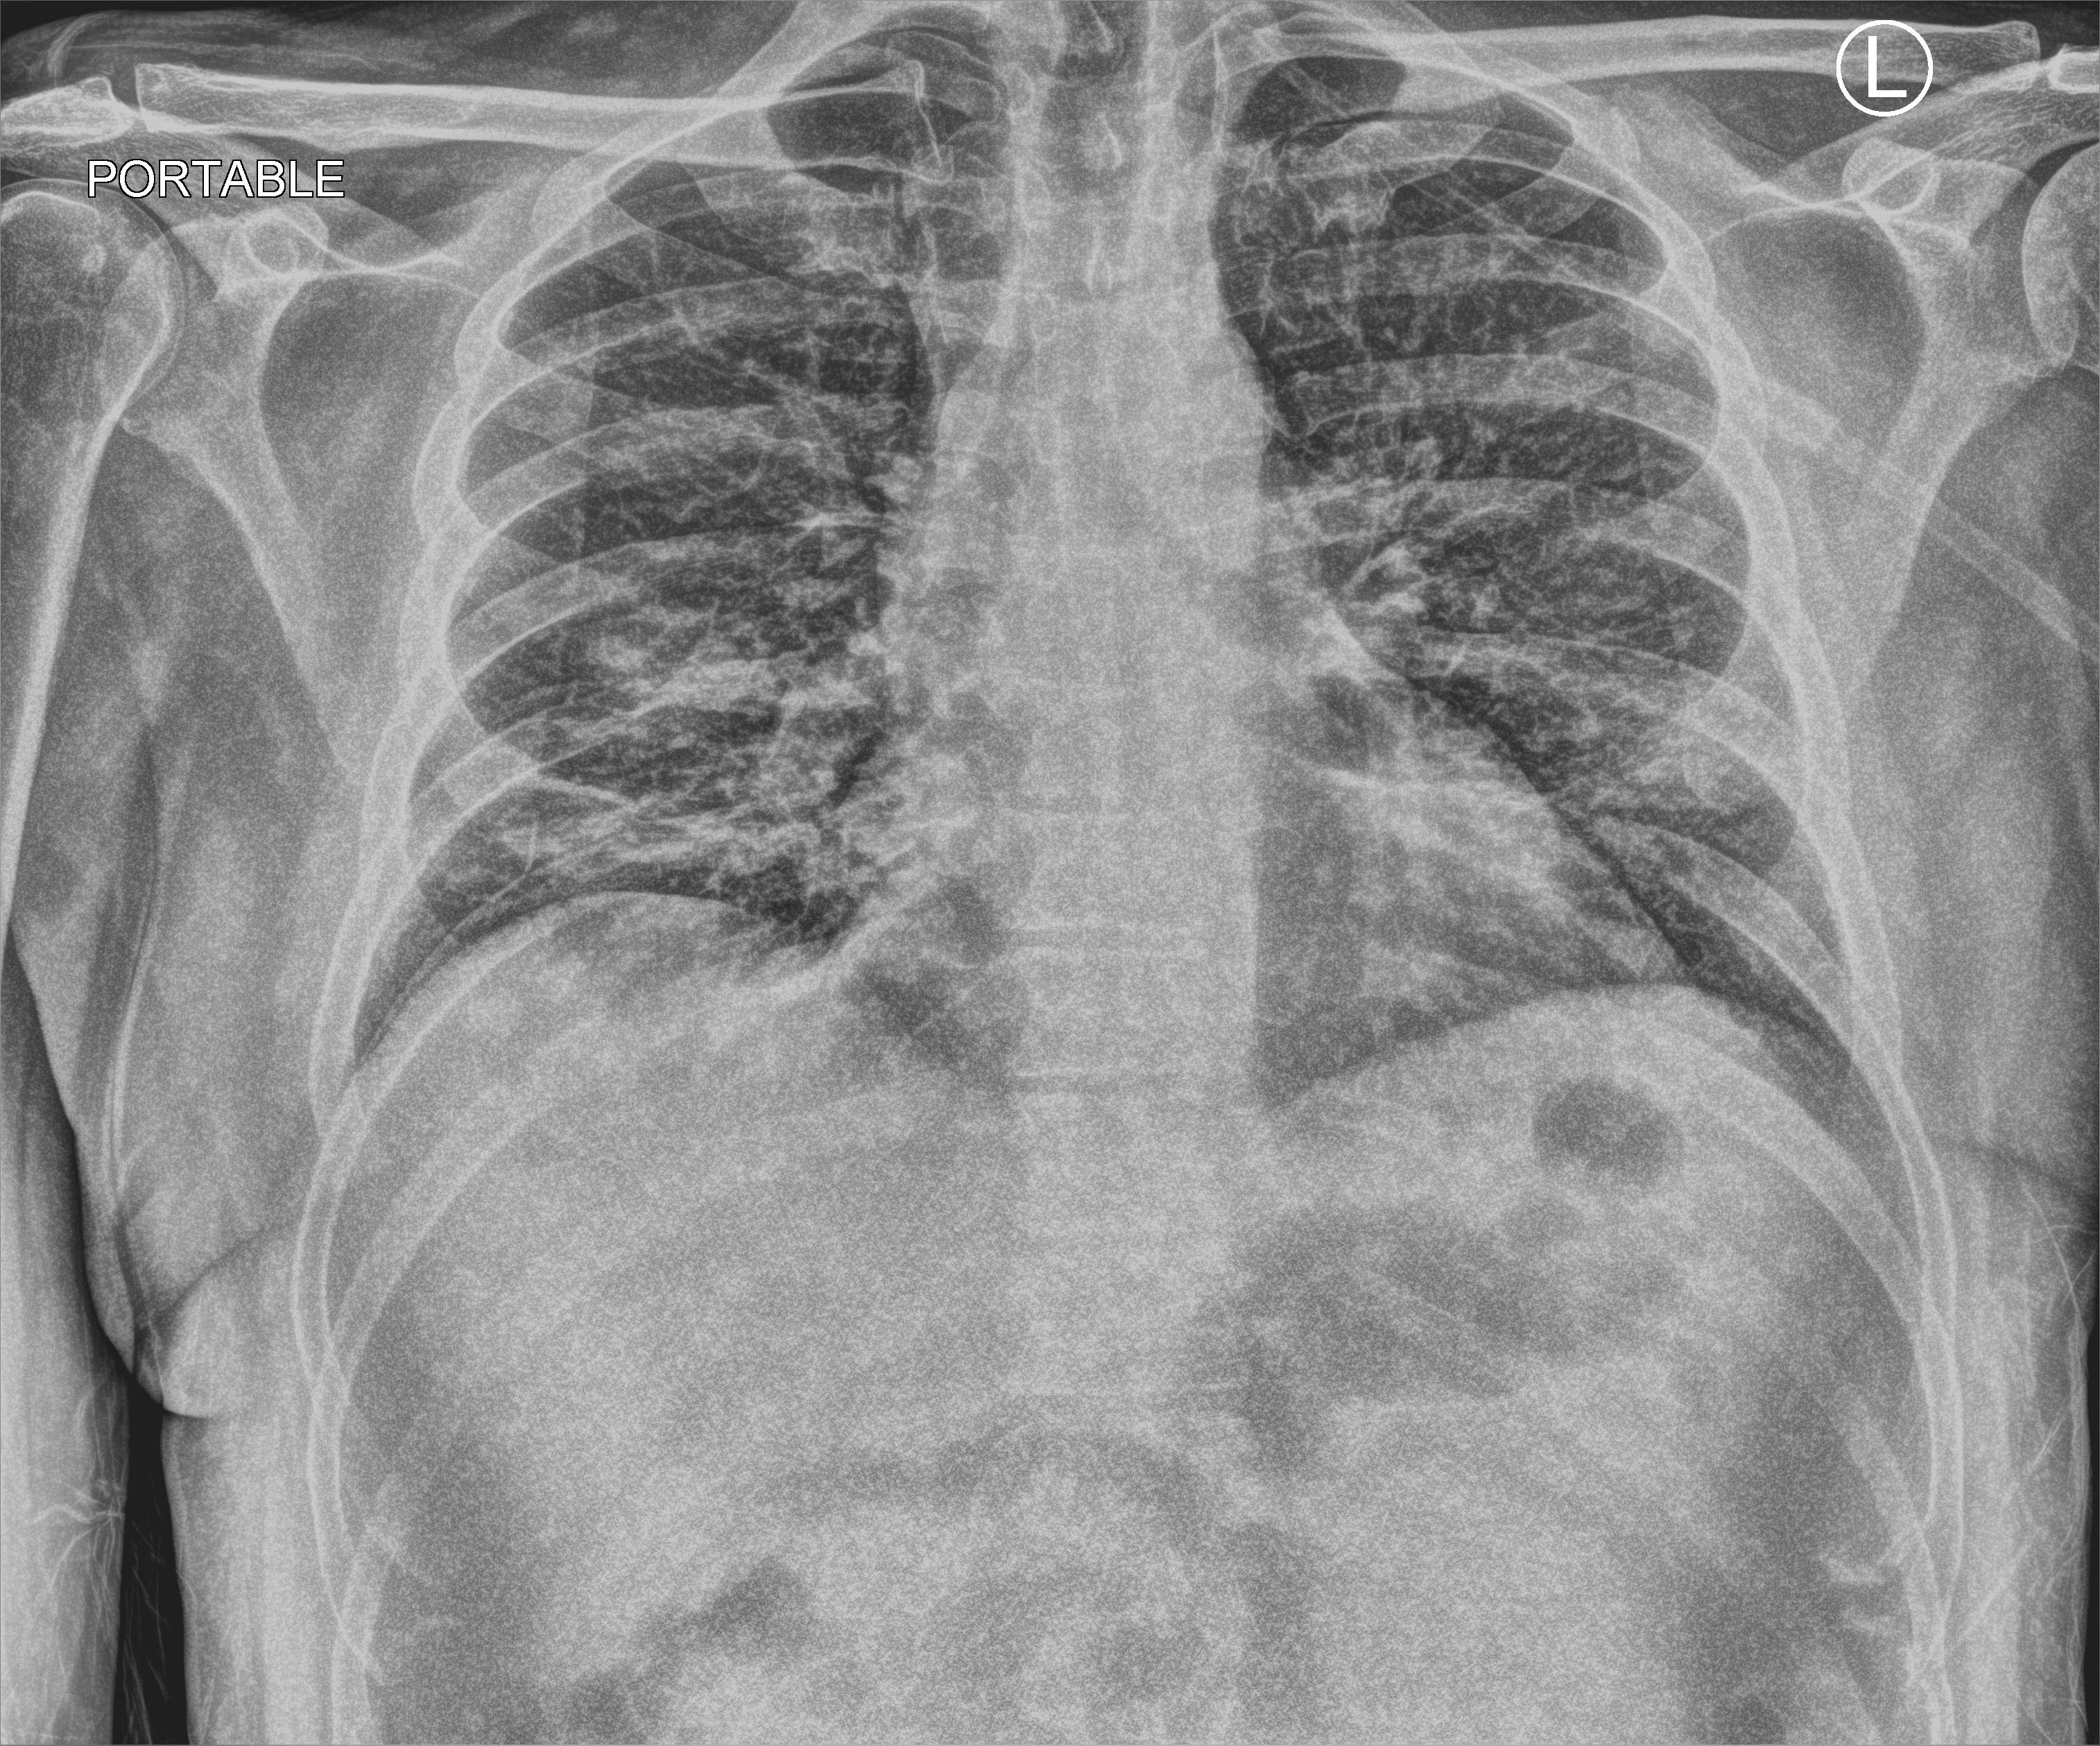
Chest X-ray (portable); anteroposterior (AP) projection. Patient hospitalised with COVID-19; male, aged 18–59 years.
From the hospital-stay record, not from the radiograph (when in the stay this image was taken is not recorded): admitted to intensive care during this hospital stay: no; mechanically ventilated during this hospital stay: no.